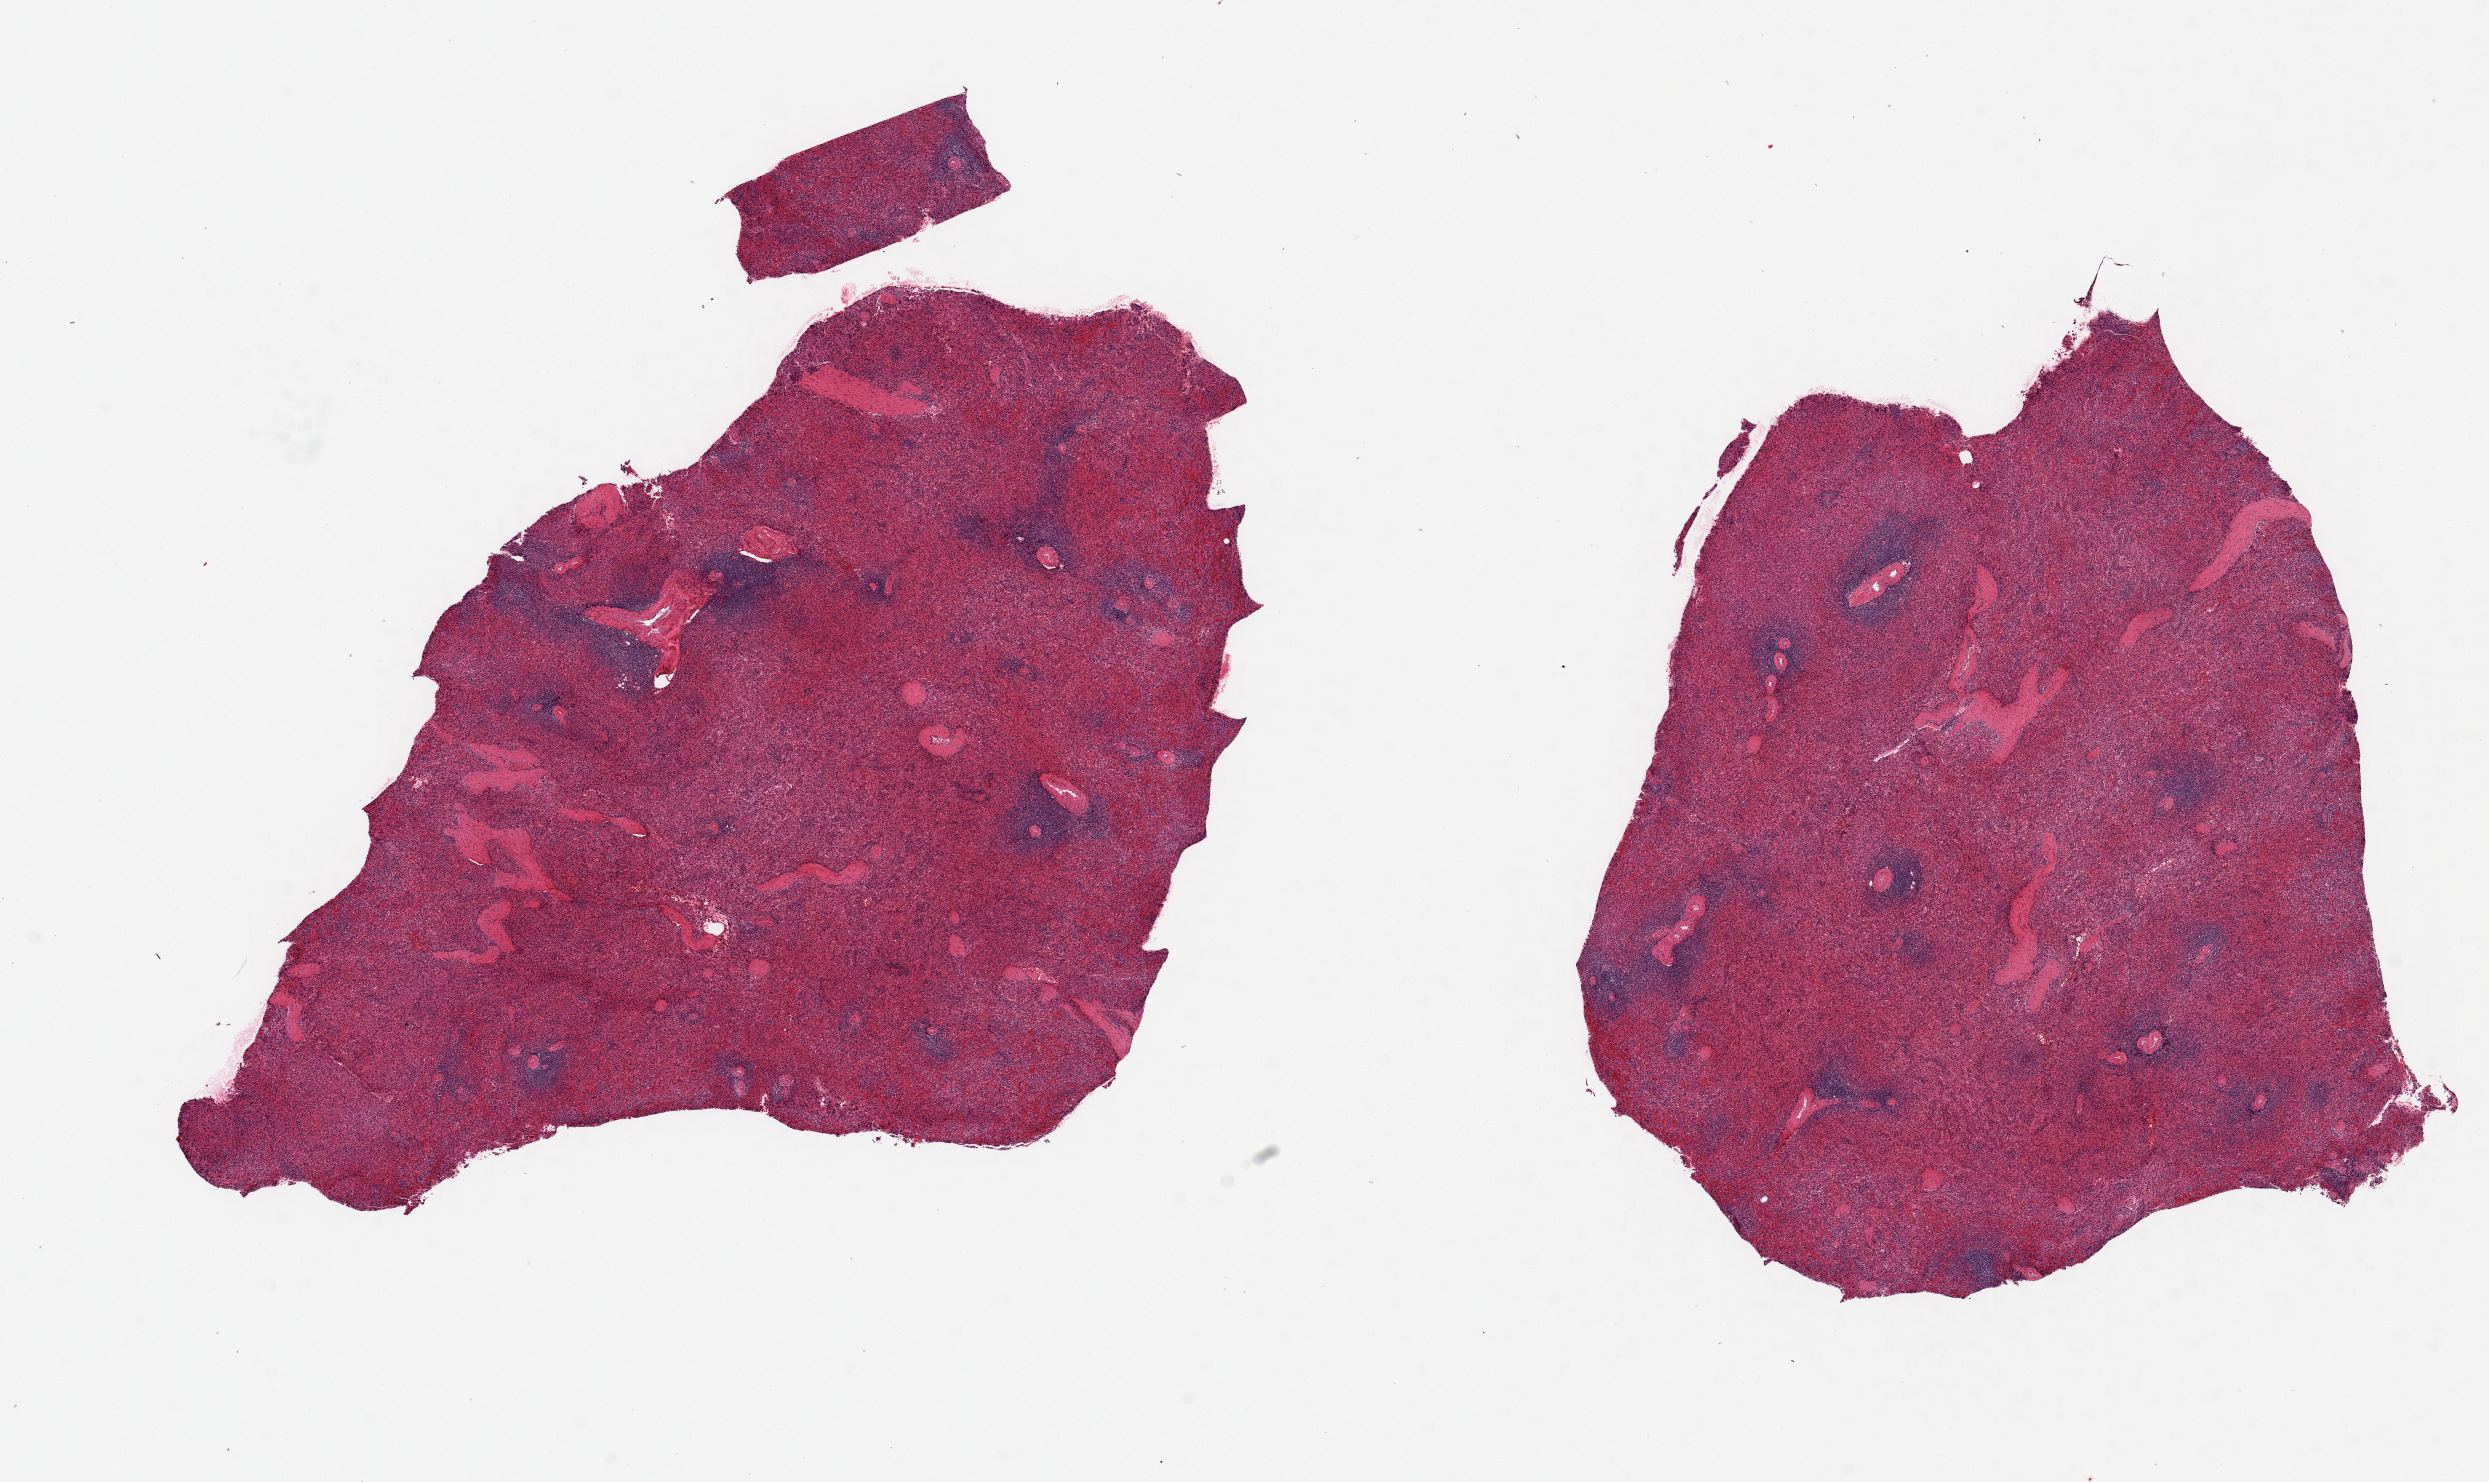
Digitized hematoxylin and eosin (H&E)-stained section, brightfield — low-resolution overview of the scanned area, about 19.7 x 11.7 mm (slide scanned at 20x), PAXgene-fixed, paraffin-embedded tissue, section of spleen (target tissue), donor tissue sample. Male donor.
Reviewer comment on this tissue sample: 2 pieces, 8.5x7 & 9x8mm; moderate congestion.